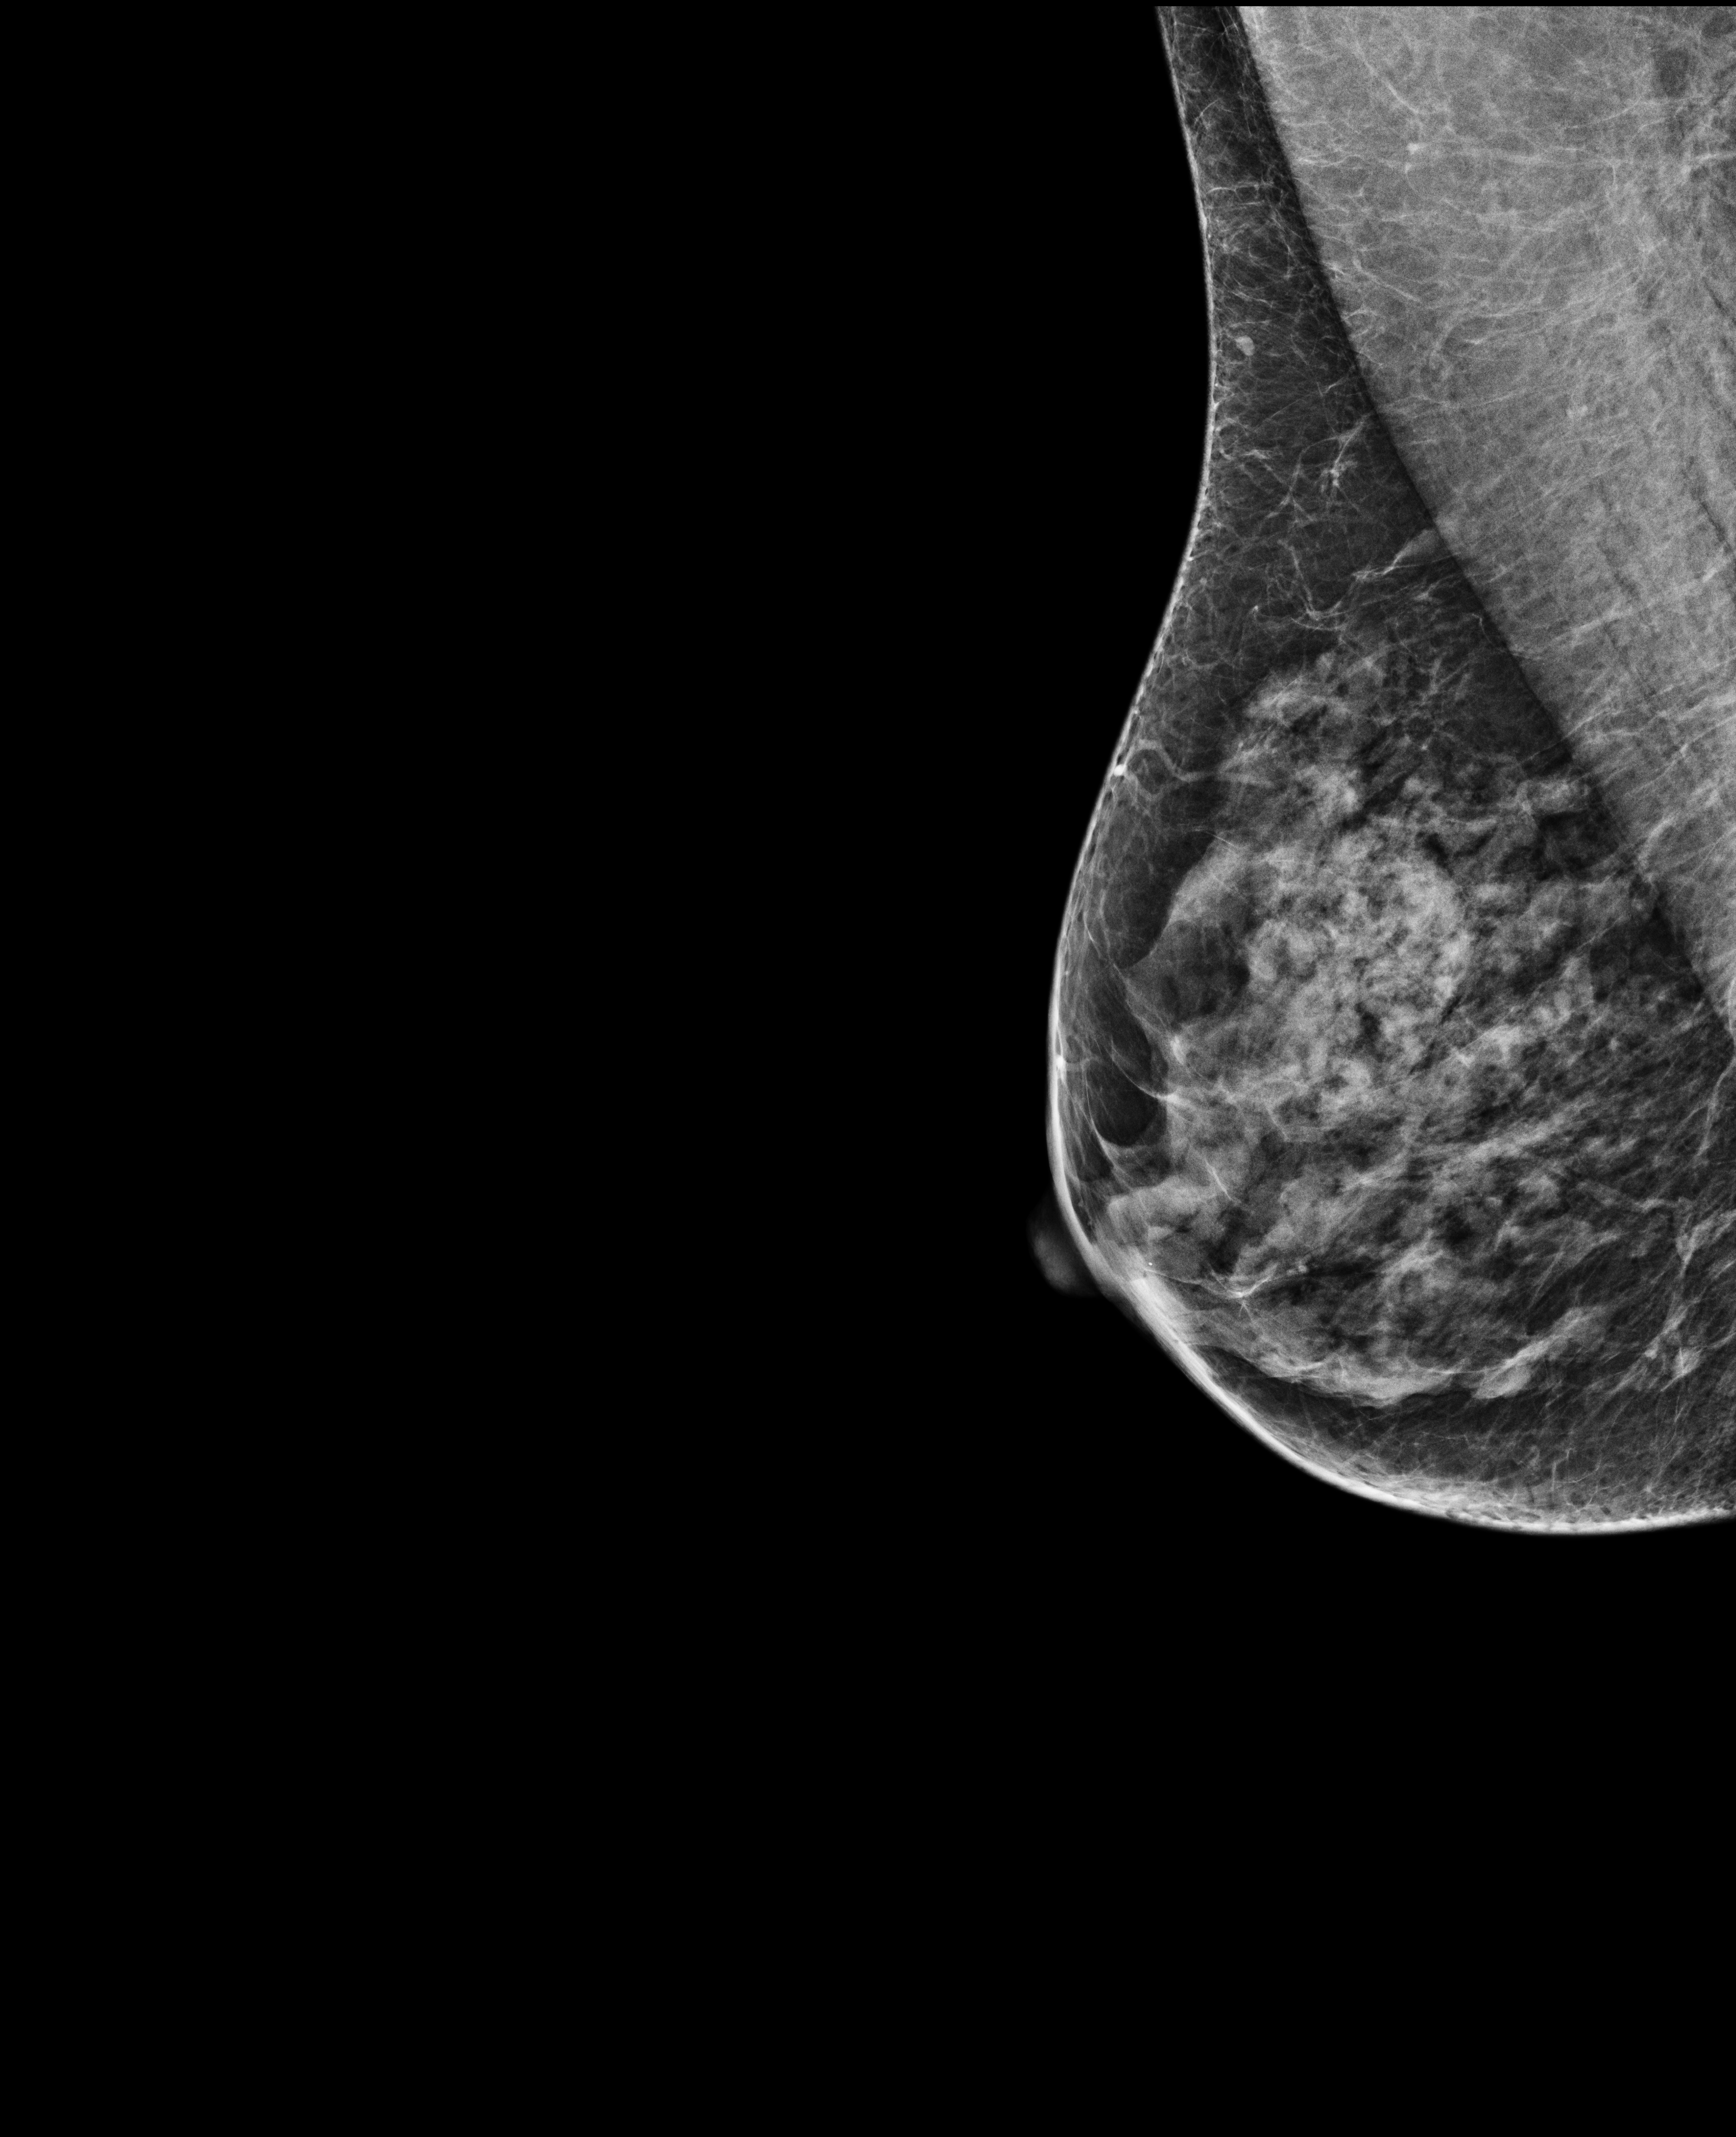
Digital mammogram (FFDM), right breast, medio-lateral oblique projection, annual screening mammography examination. Patient: female, 66 years.
Final BI-RADS assessment for this screening round (tomosynthesis exam, both breasts): category 1.